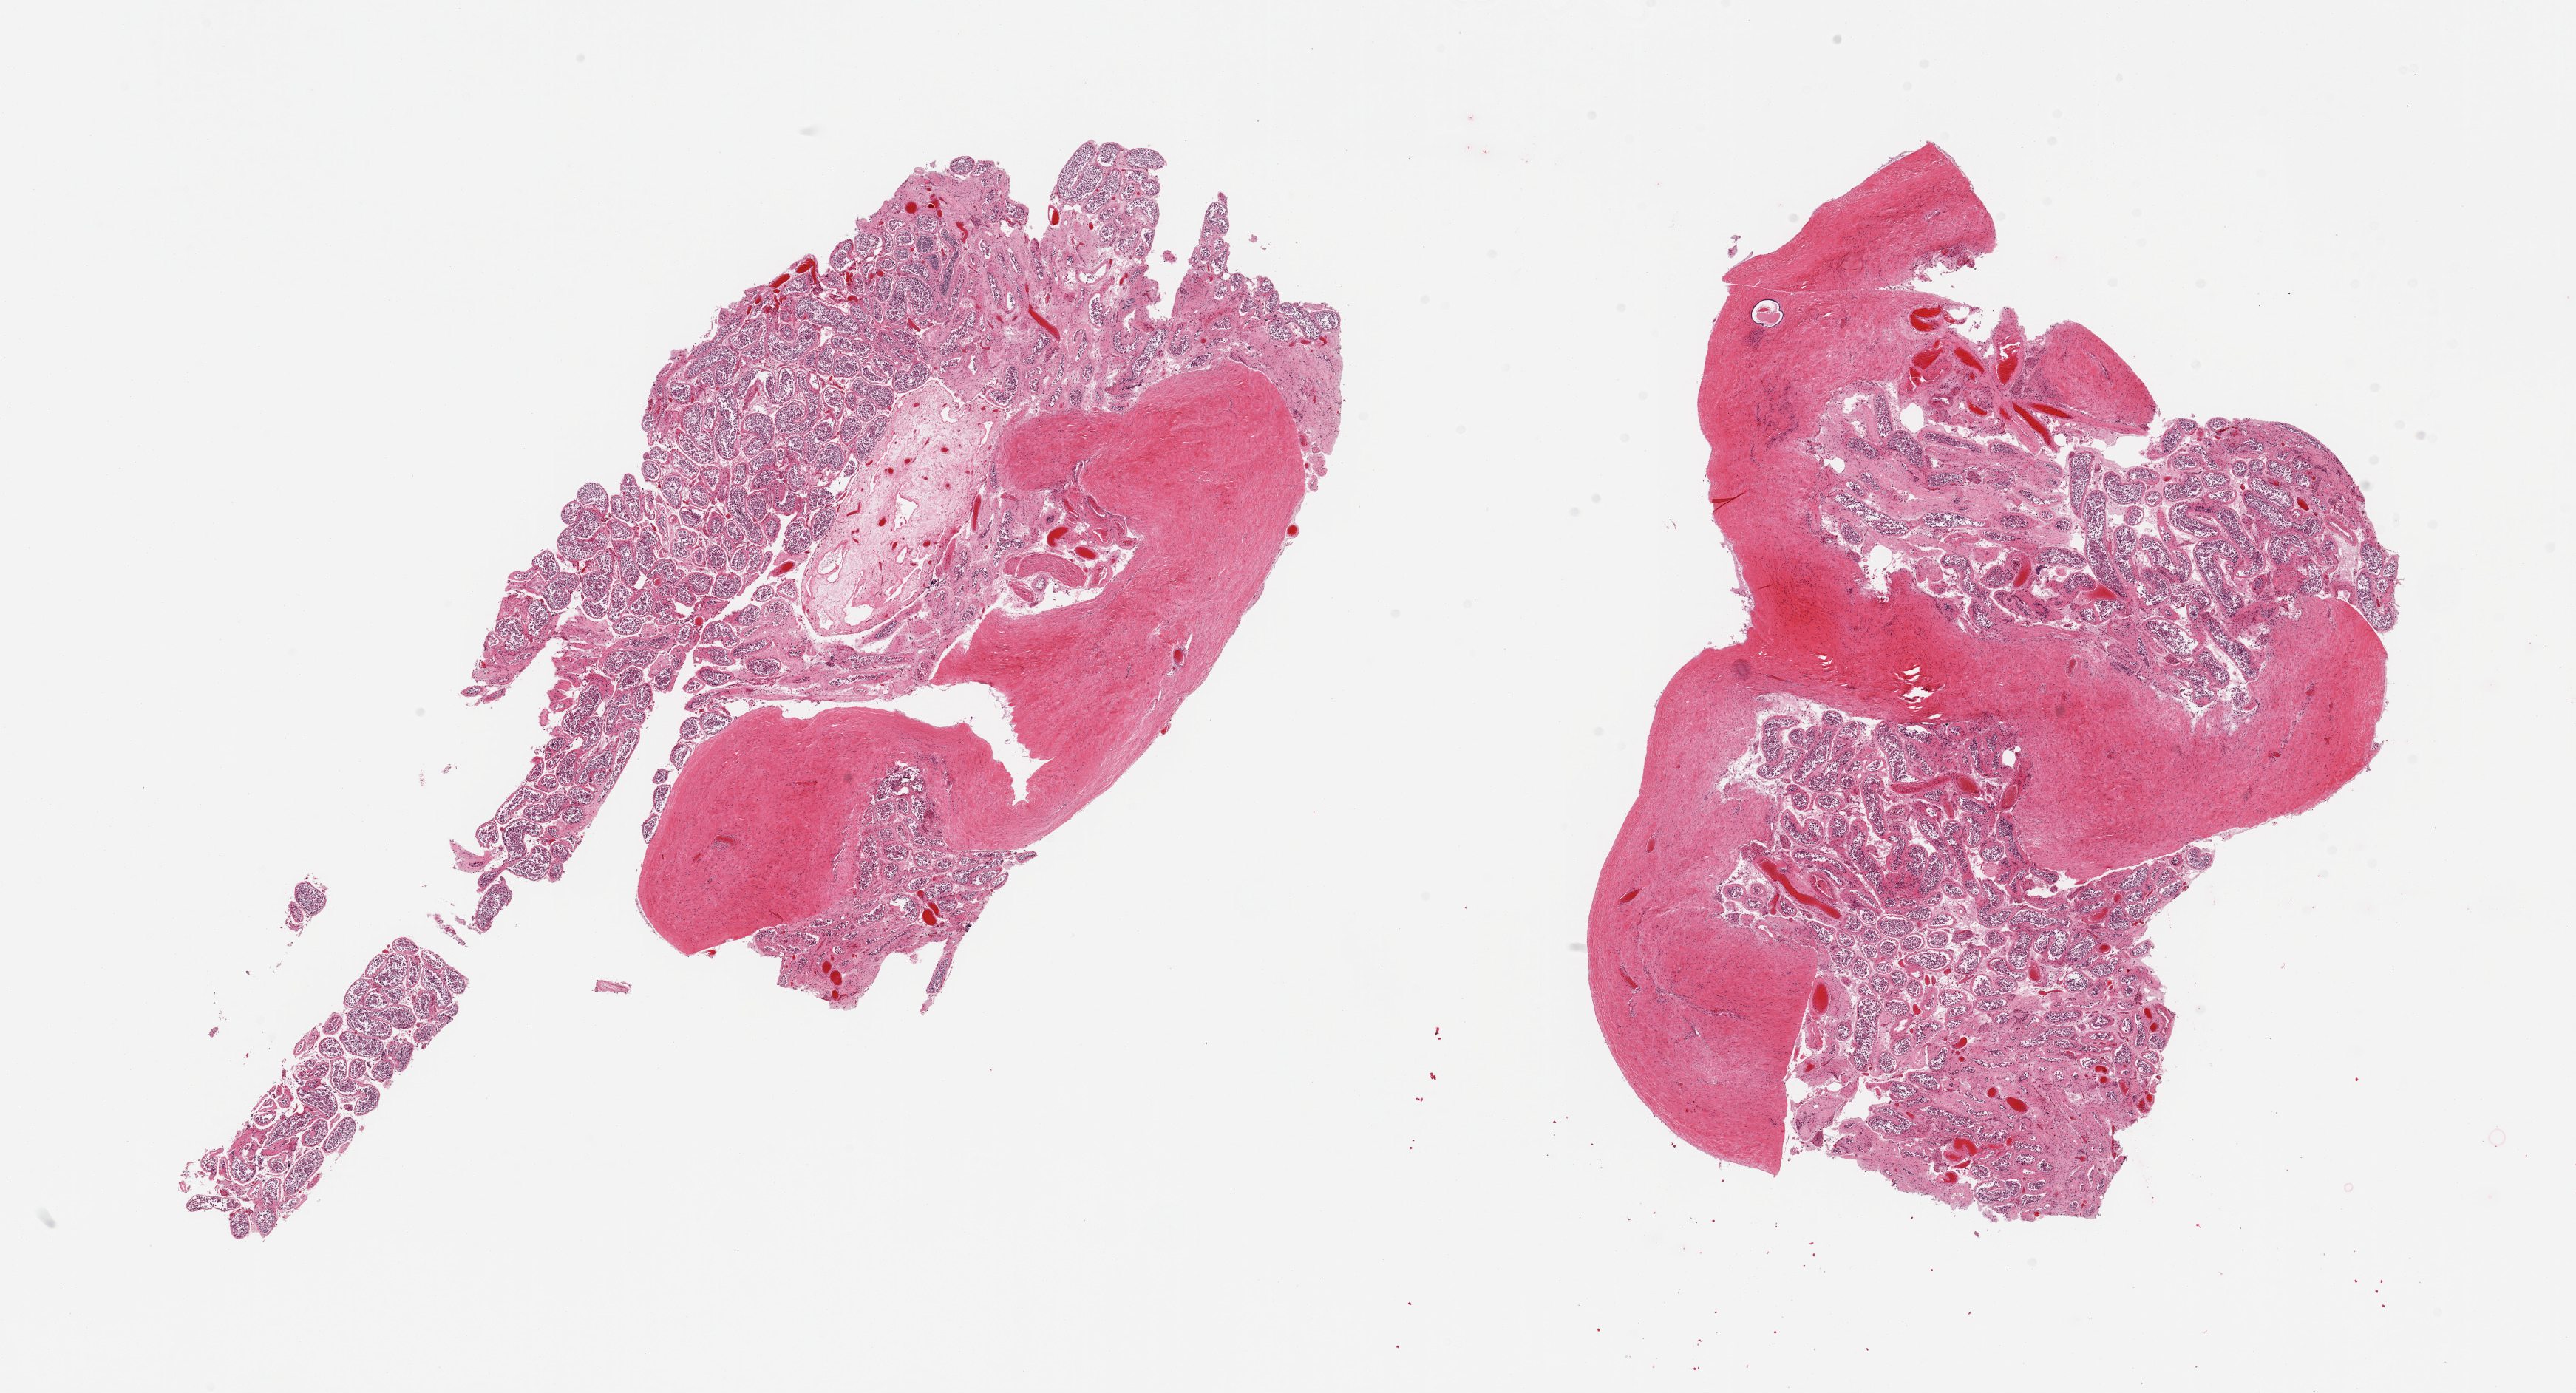
H&E whole-slide image, shown as a low-resolution overview of the whole scanned area (about 27.6 x 14.9 mm), PAXgene-fixed, paraffin-embedded tissue, section of testis (target tissue), tissue donor sample. Donor sex: male.
Pathologist's review note for this sample: 2 pieces; spermatogenesis present, some atrophy, 40% and 30% tunica albuginea.